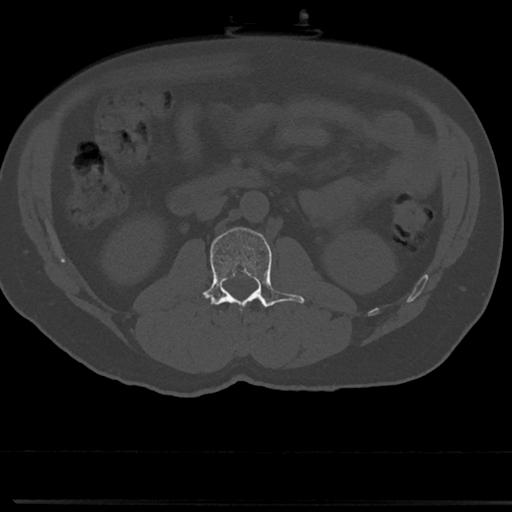
CT including the spine, one axial slice; slice 17 of 817 in the series (ordered by position); bone window (W 1800 / L 400 HU); 0.5 mm slice thickness; 512 × 512 image matrix, field of view 355 × 355 mm. Male patient, age 61 years. From the clinical record (not read from this slice): primary cancer: prostate.
Structures marked on this image (semi-automatic segmentation, software-assisted and operator-edited):
- L2 vertebra: box from (x=204, y=227) to (x=304, y=313) px